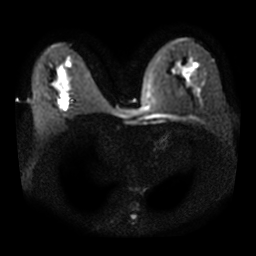
Breast MRI, one axial slice. Diffusion-weighted series; image 2 of 4 stored at this slice position (different b-values; order by instance number). 3 T. 256 × 256 image matrix. Female patient.
Structures marked on this image (outlined manually by an expert reader):
- tumour on diffusion-weighted imaging: box from (x=60, y=98) to (x=67, y=103) px